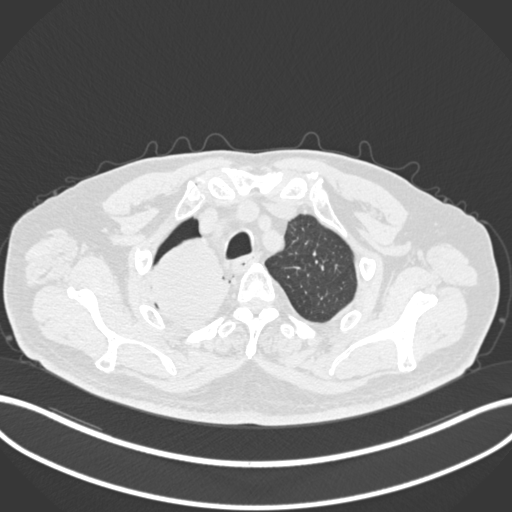
Chest CT, one axial slice; slice 182 of 218 in the series (ordered by position); lung window (W 1500 / L -600 HU); 512 × 512 image matrix. Male patient, age 68 years. Case-level facts recorded for this patient, not image findings: clinical TNM (as recorded): T2a N0 M0.
Structures marked on this image (bounding box drawn by a radiologist):
- lung tumour (recorded histology: adenocarcinoma): bounding box <147,235,232,333> (left, top, right, bottom; pixels)